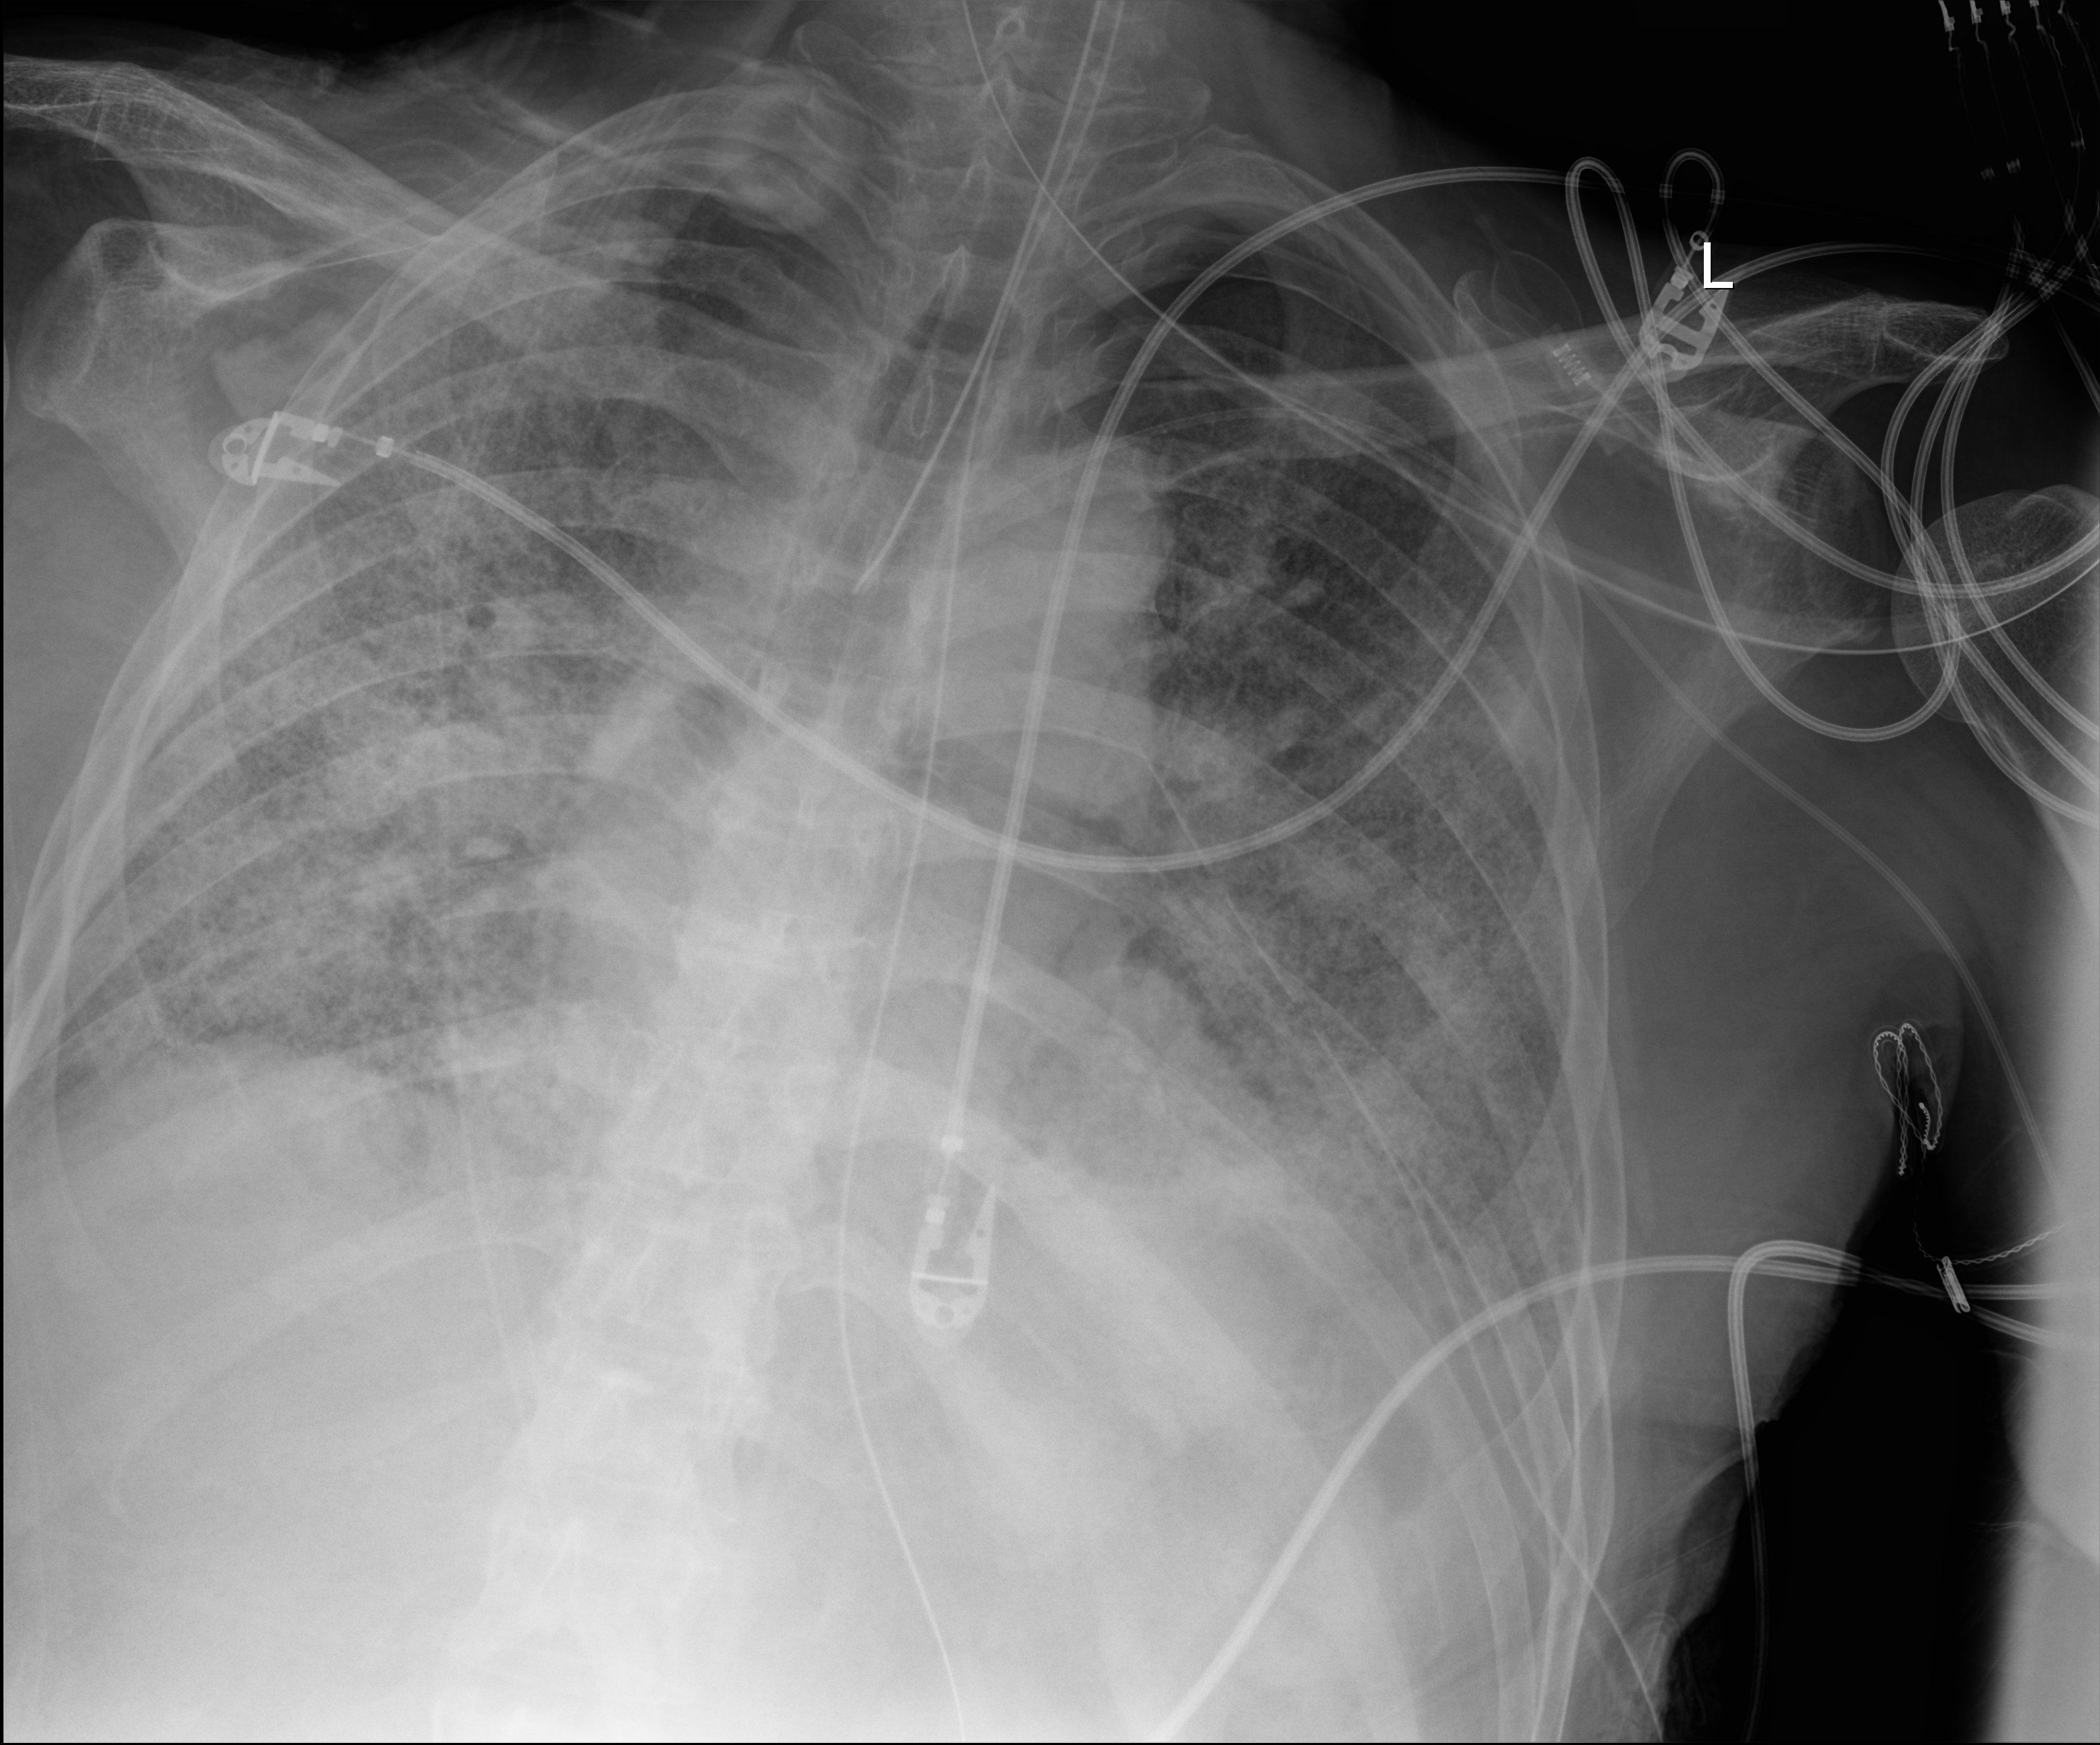
Chest radiograph (digital radiography), anteroposterior (AP) projection. Patient hospitalised with COVID-19; male, aged 60–74 years.
Hospital-stay facts (about this admission, not read from this image; timing relative to this image not recorded):
- mechanically ventilated during this hospital stay: yes
- admitted to intensive care during this hospital stay: yes